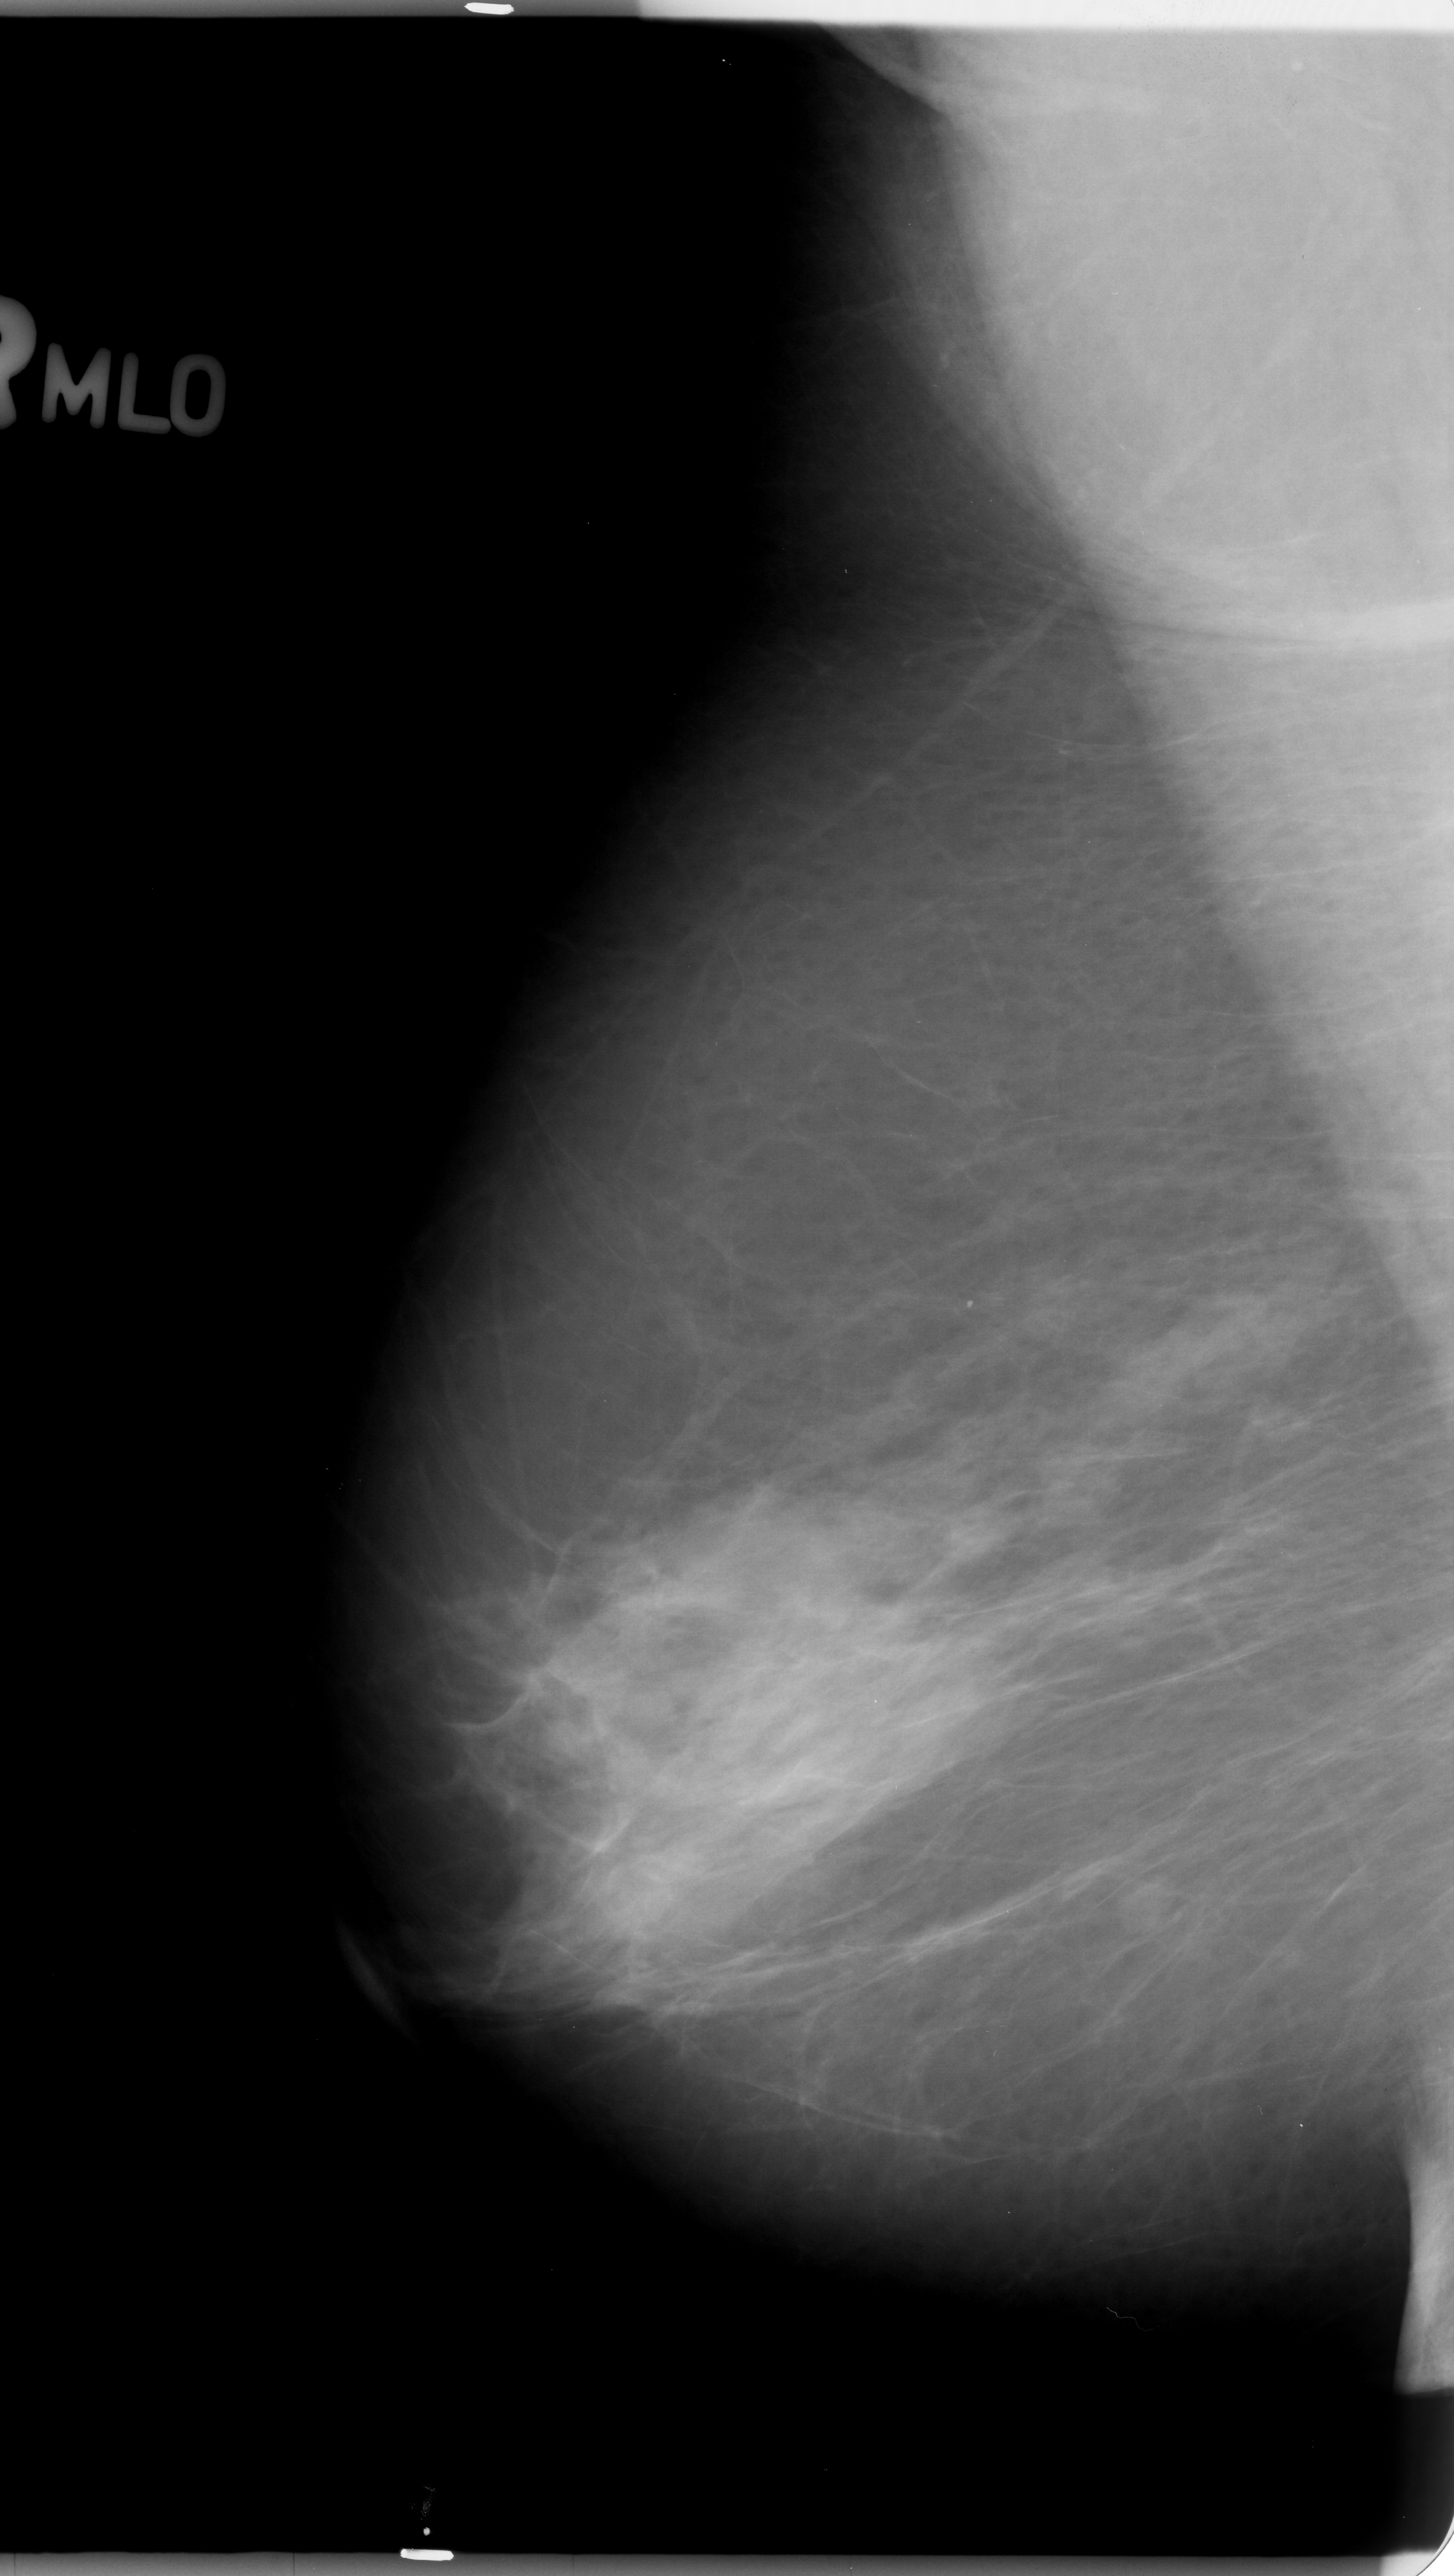
Digitized screen-film mammogram; right breast; mediolateral oblique (MLO) view; BI-RADS breast density category 3 (scale 1–4).
Finding: mass, shape irregular, margins ill defined; BI-RADS assessment category 4; pathology (as recorded): benign.